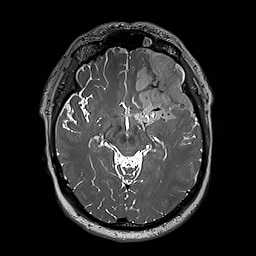
Brain MRI from a brain-tumour surgery series, one axial slice. Position 122 of 192 along the scan axis. 256 × 256 image matrix, field of view 250 × 250 mm. Case-level facts recorded for this patient, not image findings: histopathology: Oligodendroglioma; WHO grade: 3; IDH mutation: yes; tumour location: Left Sylvian Fissure (Temporal).
Annotated regions visible in this slice (manually delineated by an expert):
- tumour: bounding box [x1, y1, x2, y2] px = [124, 52, 197, 124]